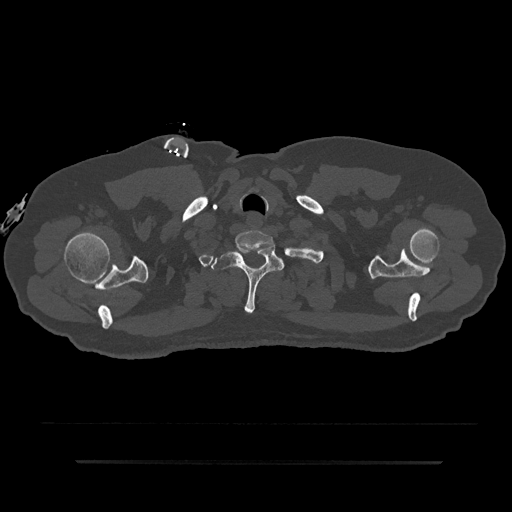
CT including the spine, one axial slice. Slice 744 of 797 in the series (ordered by position). Reconstruction kernel Br40s/3. Bone window (W 1800 / L 400 HU). 0.5 mm slice thickness. 512 × 512 image matrix, field of view 464 × 464 mm. Patient: male, 59 years. From the clinical record (not read from this slice): primary cancer: bile ducts; vertebrae with lytic lesions (as recorded): T10.
Structures marked on this image (semi-automatic segmentation, software-assisted and operator-edited):
- T1 vertebra: bounding box (x1, y1, x2, y2) in pixels: (211, 247, 284, 314)